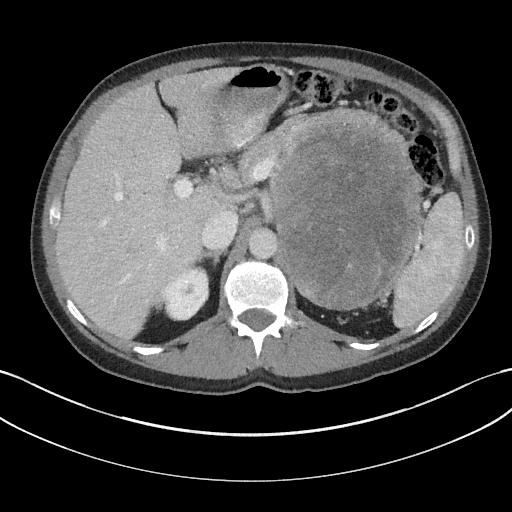
Contrast-enhanced abdominal CT, one axial slice; slice 116 of 147 in the series (ordered by position); 100 kVp; soft-tissue window (W 400 / L 40 HU); 3 mm slice thickness; 512 × 512 image matrix, field of view 384 × 384 mm. Male patient, age 58 years. From the clinical record (not read from this slice): diagnosis: adrenocortical carcinoma; tumour side: left adrenal; tumour size at pathology: 22 cm; Ki-67 index: 26 %; stage (as recorded): 2.
Annotated regions visible in this slice (semi-automatic segmentation, software-assisted and operator-edited):
- mass: box from (x=273, y=127) to (x=417, y=308) px